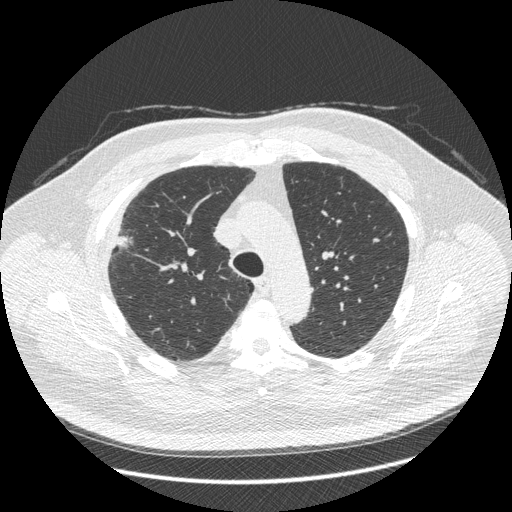
Low-dose screening chest CT, one axial slice; position 315 of 426 along the scan axis; reconstruction kernel STANDARD; 120 kVp; lung window (W 1500 / L -600 HU); 1.25 mm slice thickness; 512 × 512 image matrix.
Outlined on this slice (manually delineated by an expert):
- lesion 1 (tumor, upper lobe of right lung): bounding box <117,236,129,247> (left, top, right, bottom; pixels)